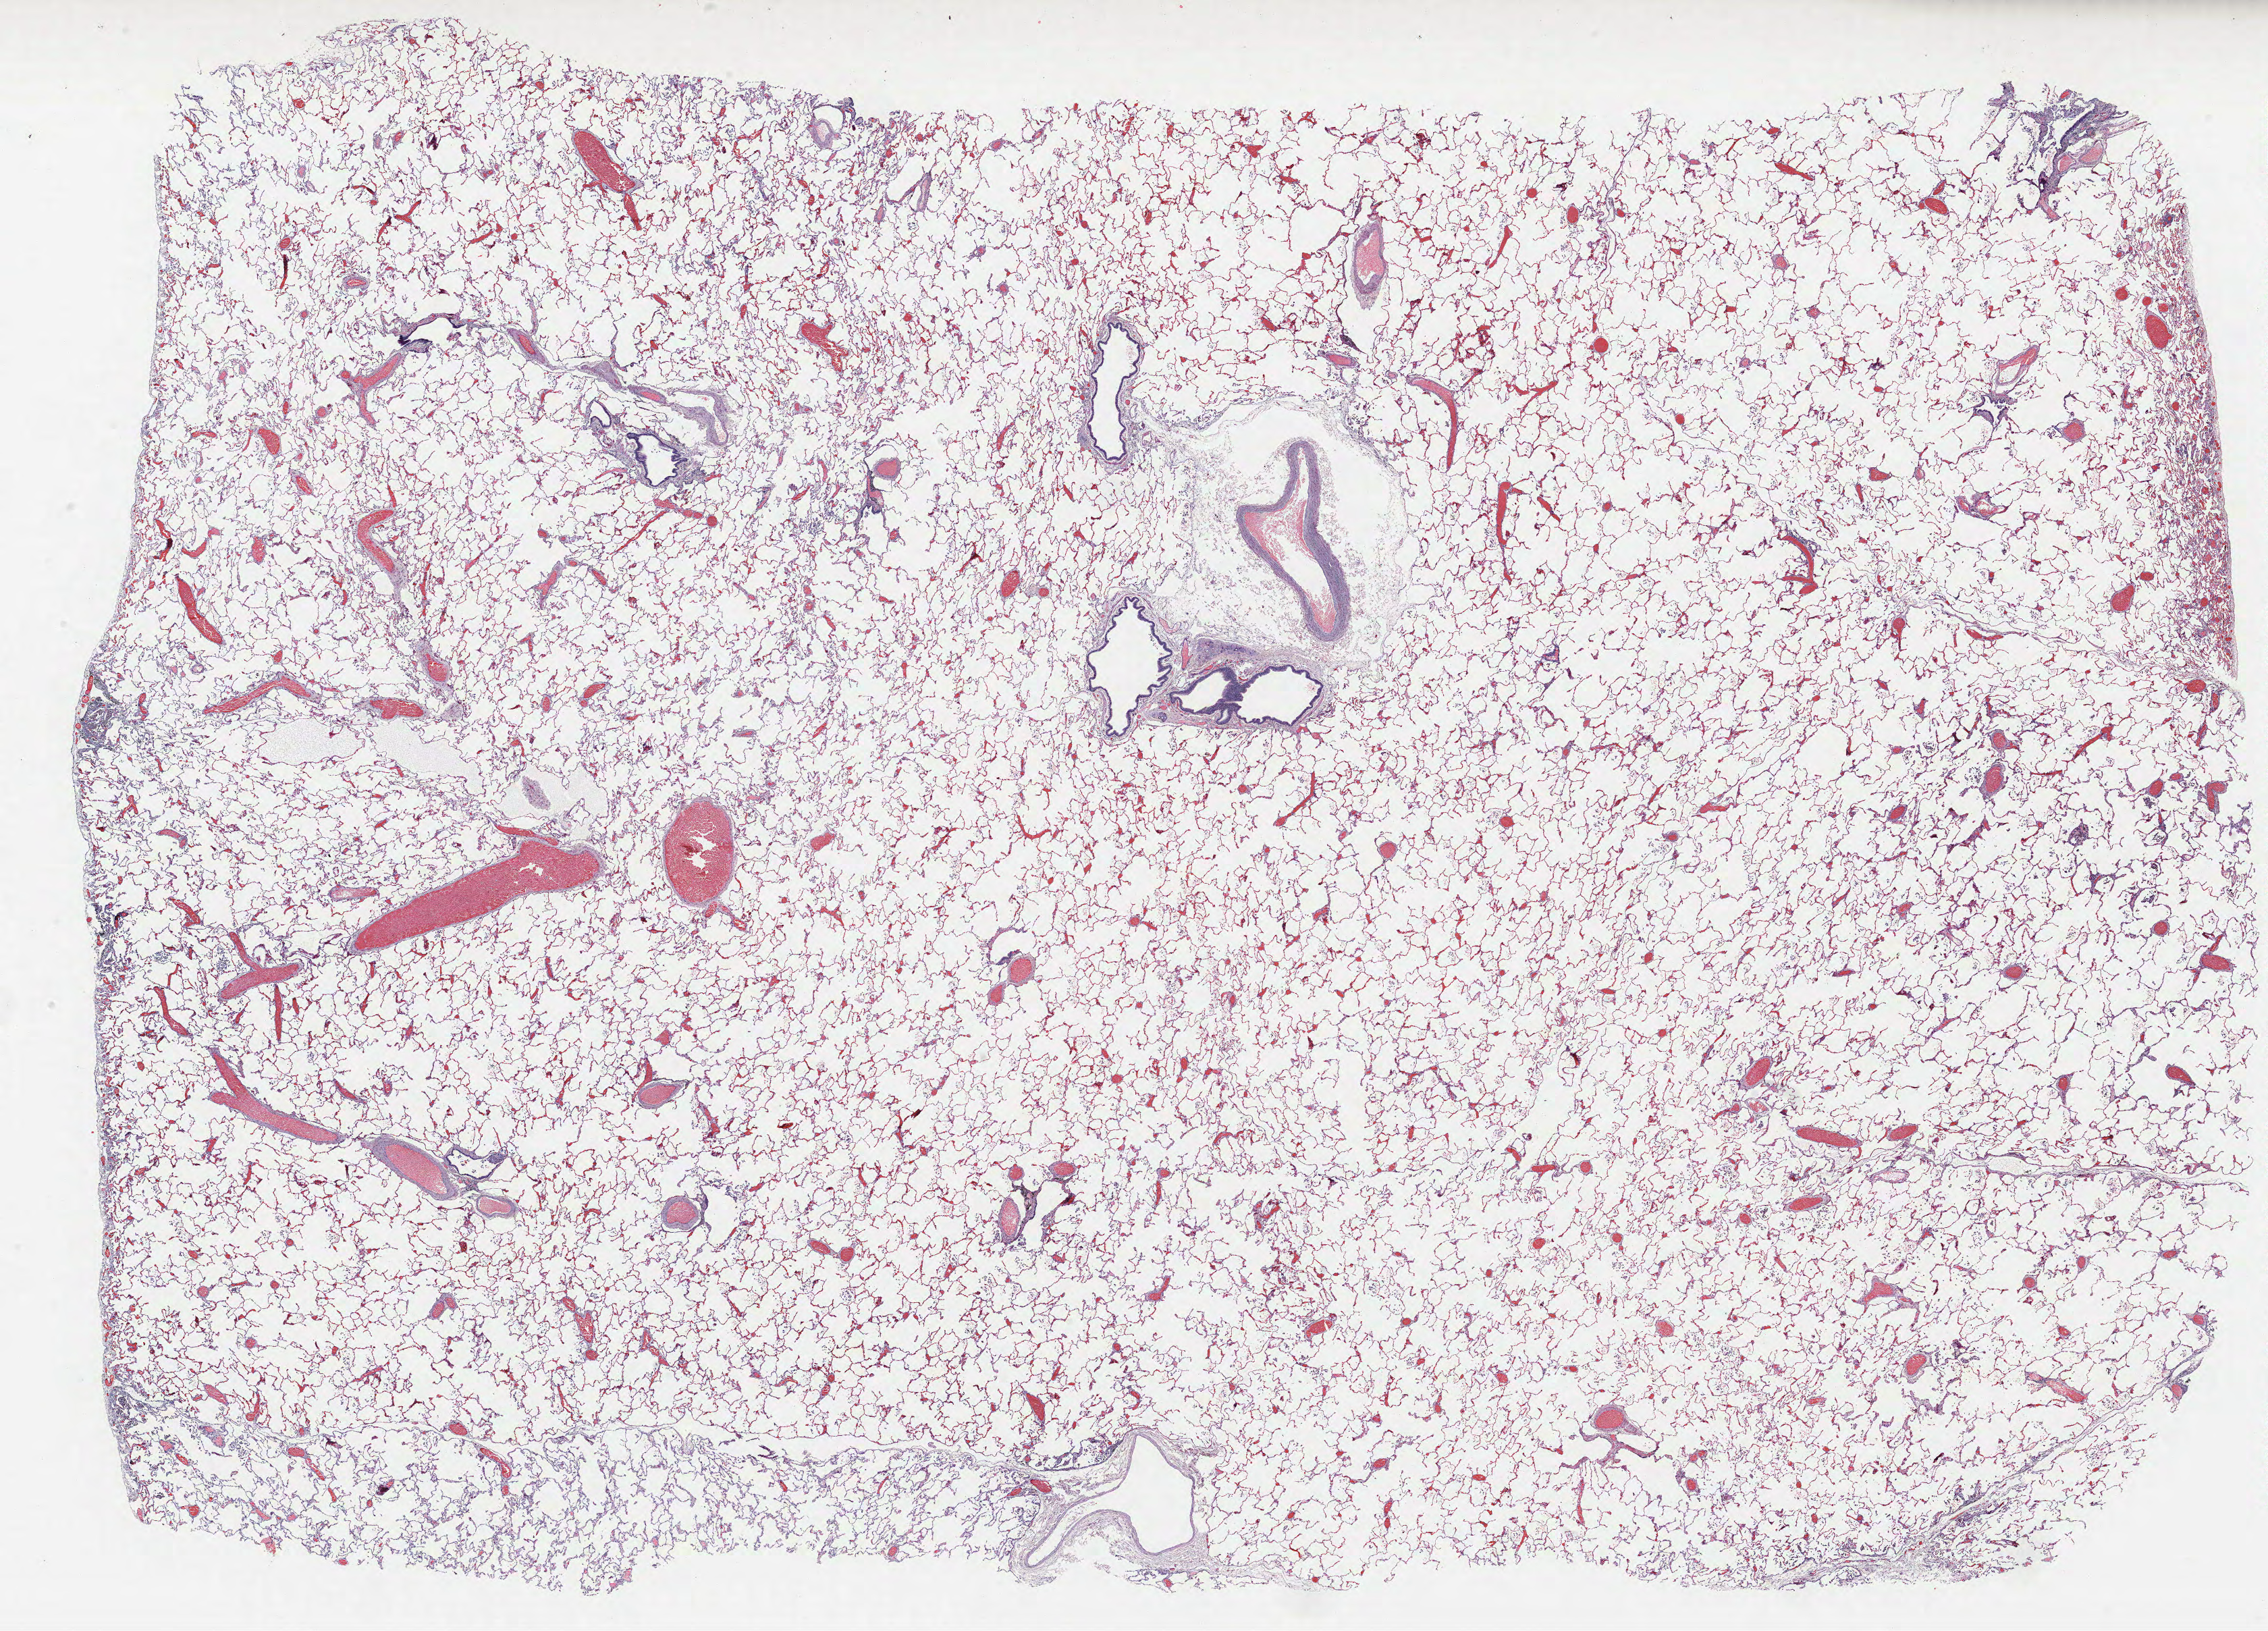
Whole-slide histology image, H&E — low-resolution overview of the scanned area, about 26.9 x 19.3 mm; FFPE section; lung. Male patient, aged 56 at enrolment. Former smoker at enrolment.
Participant's lung-cancer diagnosis: Adenocarcinoma, NOS.